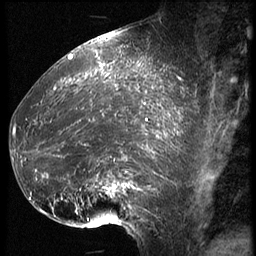
Breast MRI (dynamic contrast-enhanced), one sagittal slice. Position 25 of 62 along the scan axis. 3 images stored at this slice position (order not interpretable as contrast timing). 1.5 T. TE 4.2 ms, TR 9 ms. 2.5 mm slice thickness. 256 × 256 image matrix, field of view 180 × 180 mm. Female patient, age 39 years. From the clinical record (not read from this slice): setting: breast cancer imaged before/during neoadjuvant chemotherapy; receptor status: HER2-positive.
Outlined on this slice (semi-automatic segmentation, software-assisted and operator-edited):
- analysis volume of interest (the breast-tissue region the enhancement analysis was run in; not a lesion): bounding box [x1, y1, x2, y2] px = [16, 64, 171, 228]
- tumour enhancement mask (voxels above the 140 % enhancement threshold inside the analysis volume of interest): [25, 64, 171, 207]